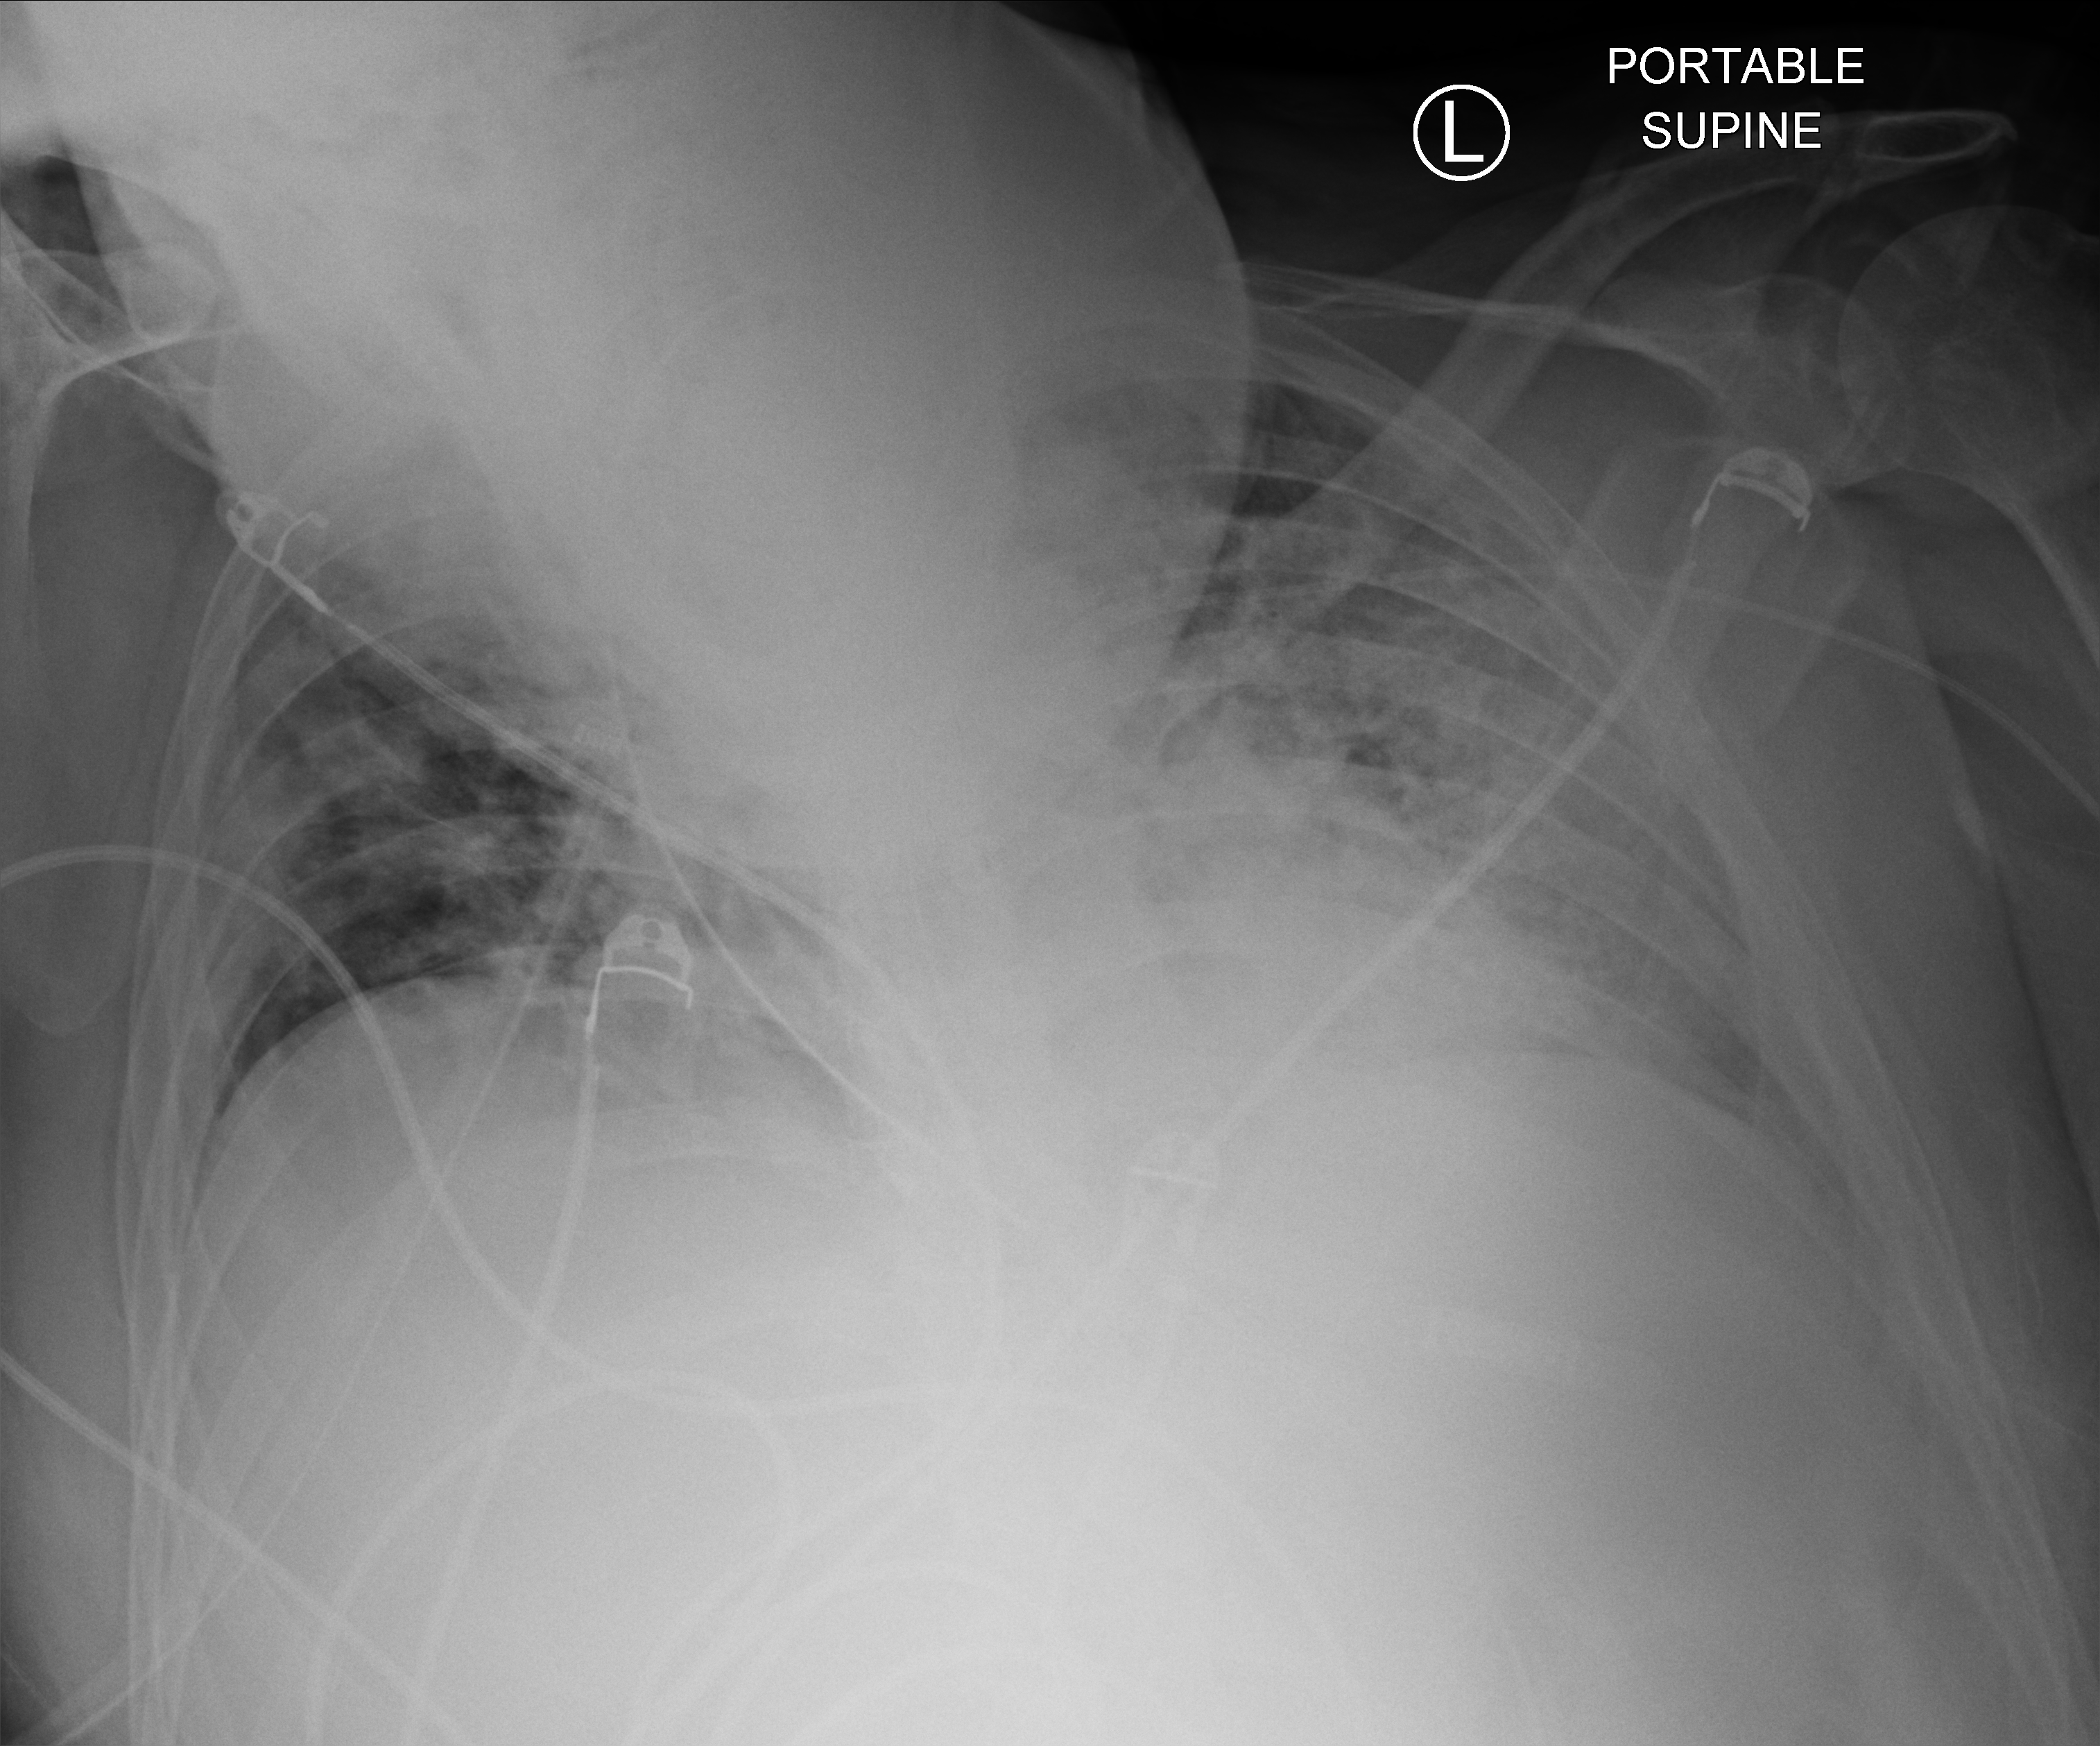
Bedside chest radiograph (computed radiography), anteroposterior (AP) projection. Male patient hospitalised with COVID-19, age 18–59 years.
From the hospital-stay record, not from the radiograph (when in the stay this image was taken is not recorded): admitted to intensive care during this hospital stay: yes; mechanically ventilated during this hospital stay: yes.